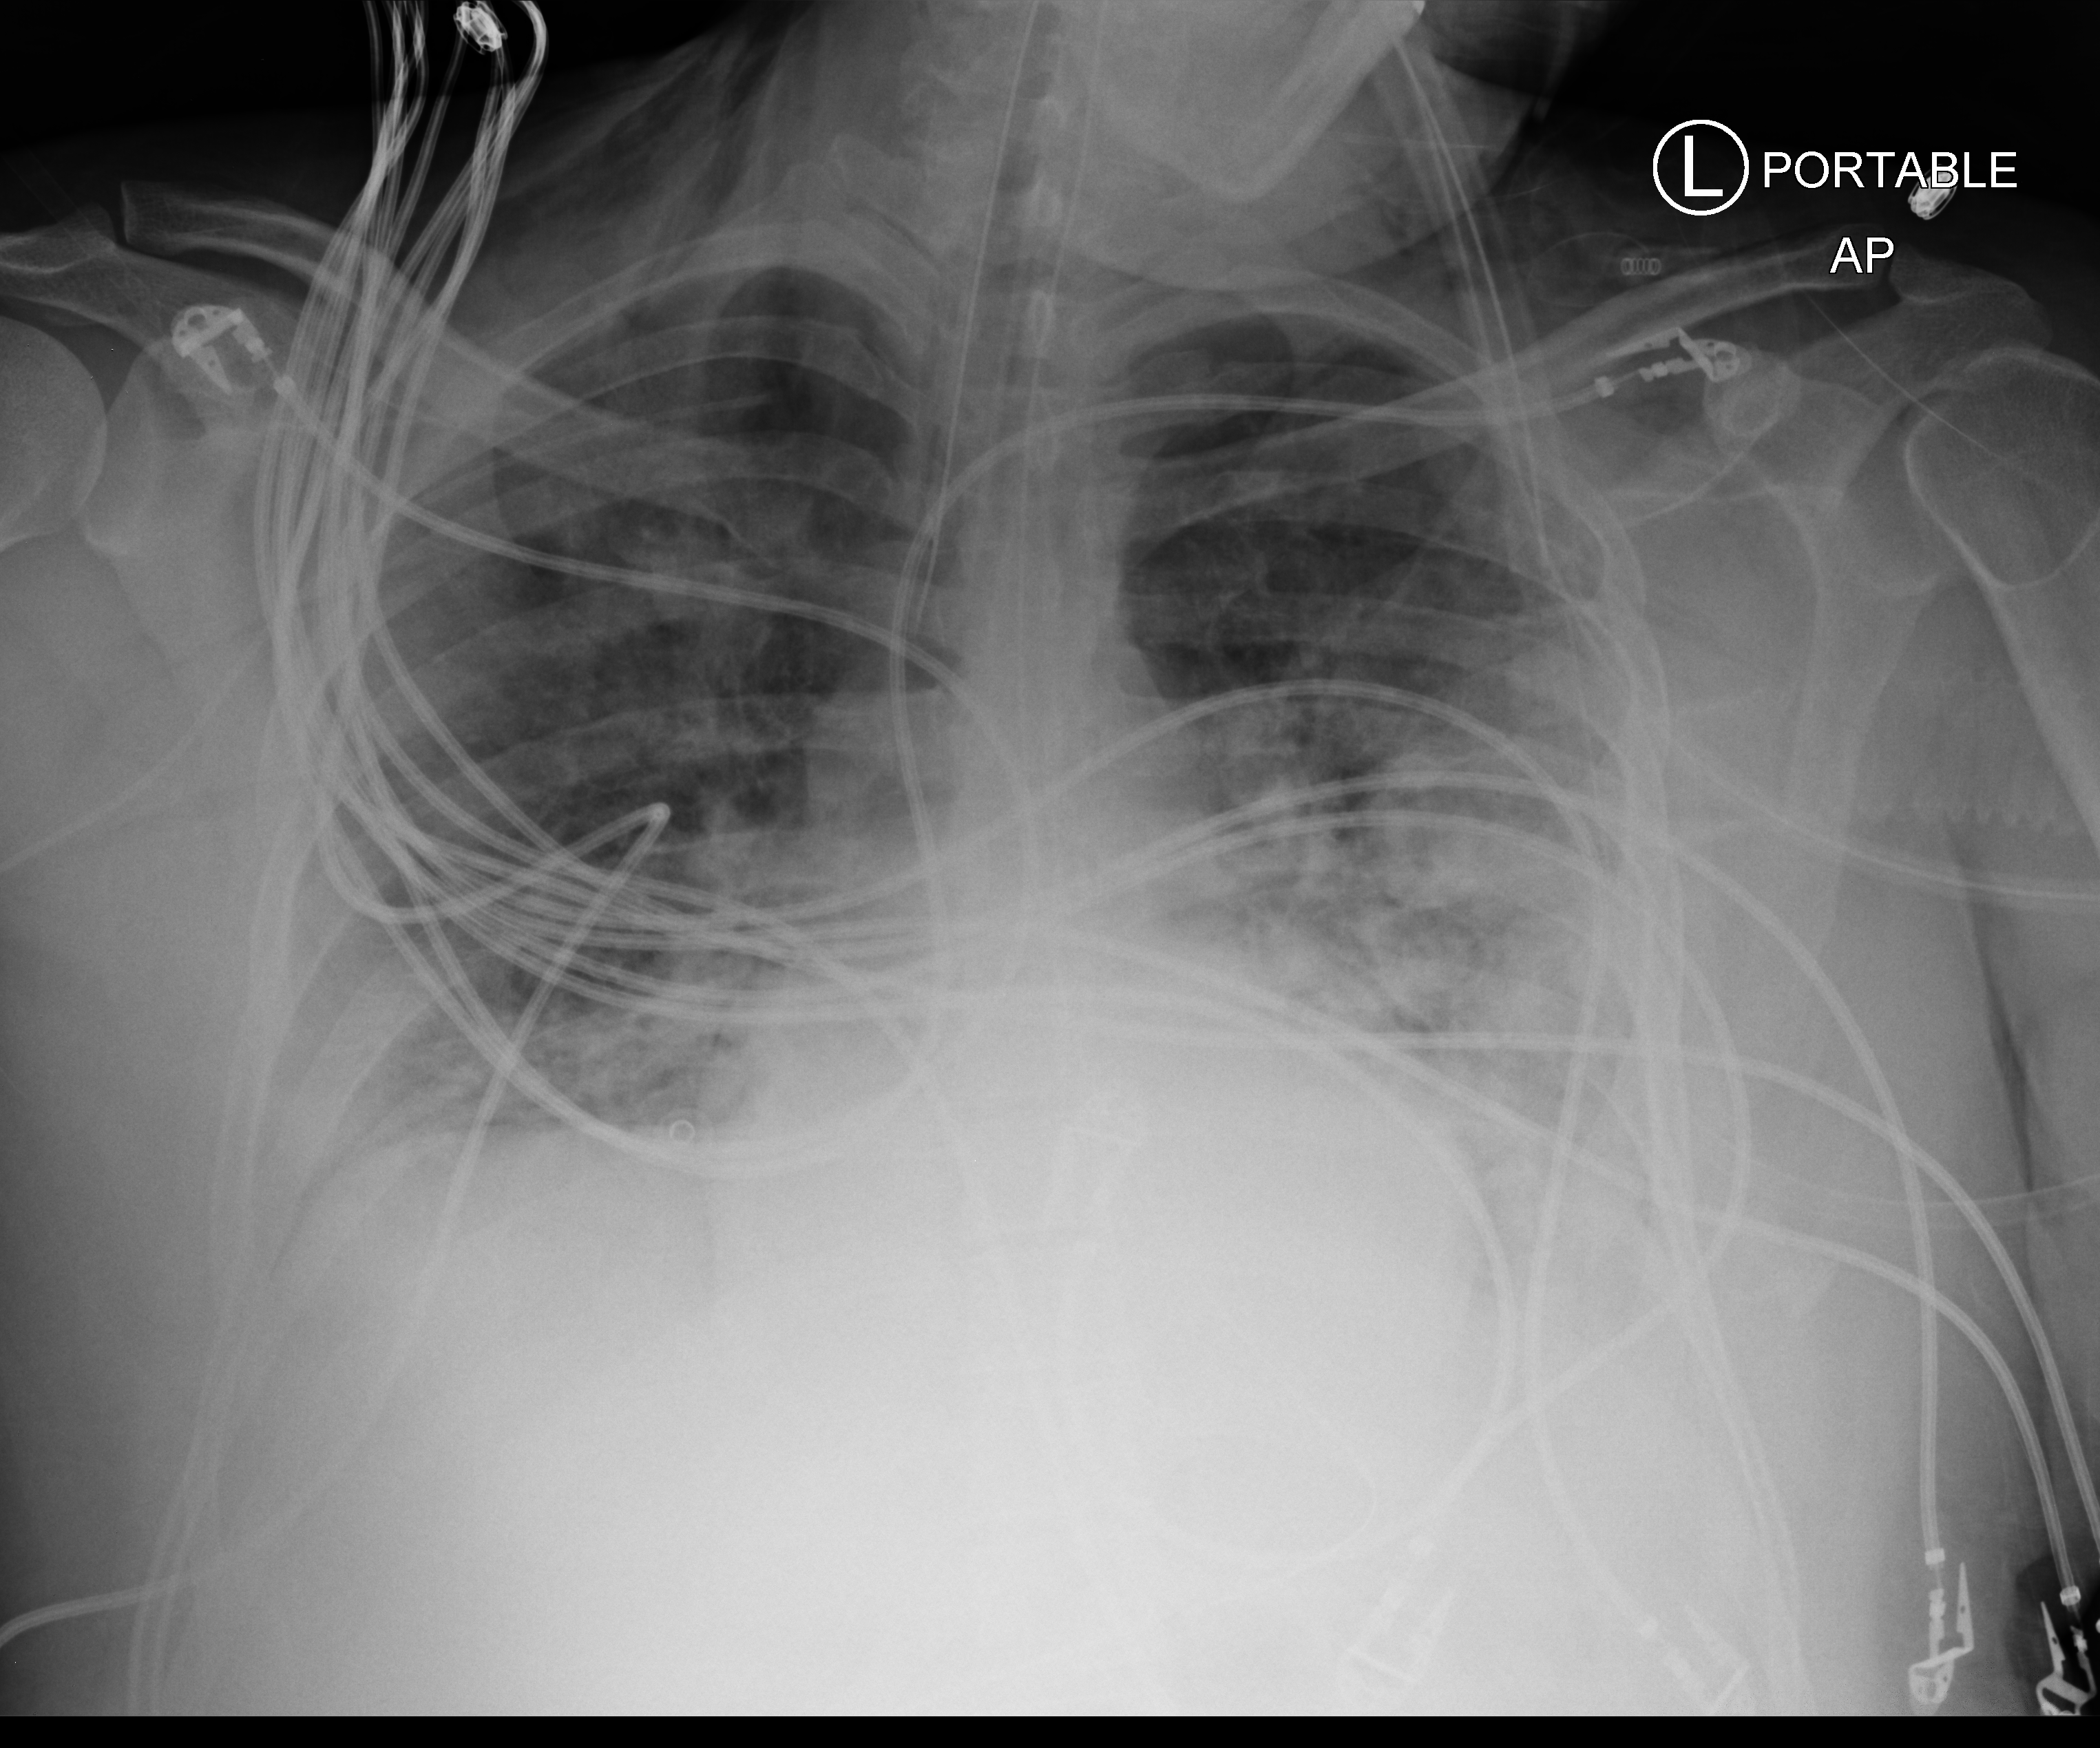
Portable chest radiograph, anteroposterior (AP) projection. Male patient hospitalised with COVID-19, age 18–59 years.
Hospital-stay facts (about this admission, not read from this image; timing relative to this image not recorded):
- other chronic lung disease (admission record): no
- mechanically ventilated during this hospital stay: yes